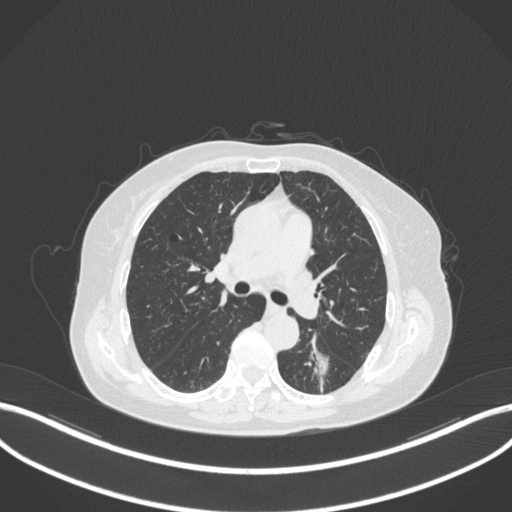
Chest CT, one axial slice; slice 178 of 352 in the series (ordered by position); reconstruction kernel B31f; lung window (W 1500 / L -600 HU); 1 mm slice thickness; 512 × 512 image matrix, field of view 400 × 400 mm. Female patient, age 70 years. Case-level facts recorded for this patient, not image findings: clinical TNM (as recorded): T1c N0 M0.
Annotated regions visible in this slice (bounding box drawn by a radiologist):
- lung tumour (recorded histology: adenocarcinoma): box from (x=305, y=334) to (x=337, y=386) px